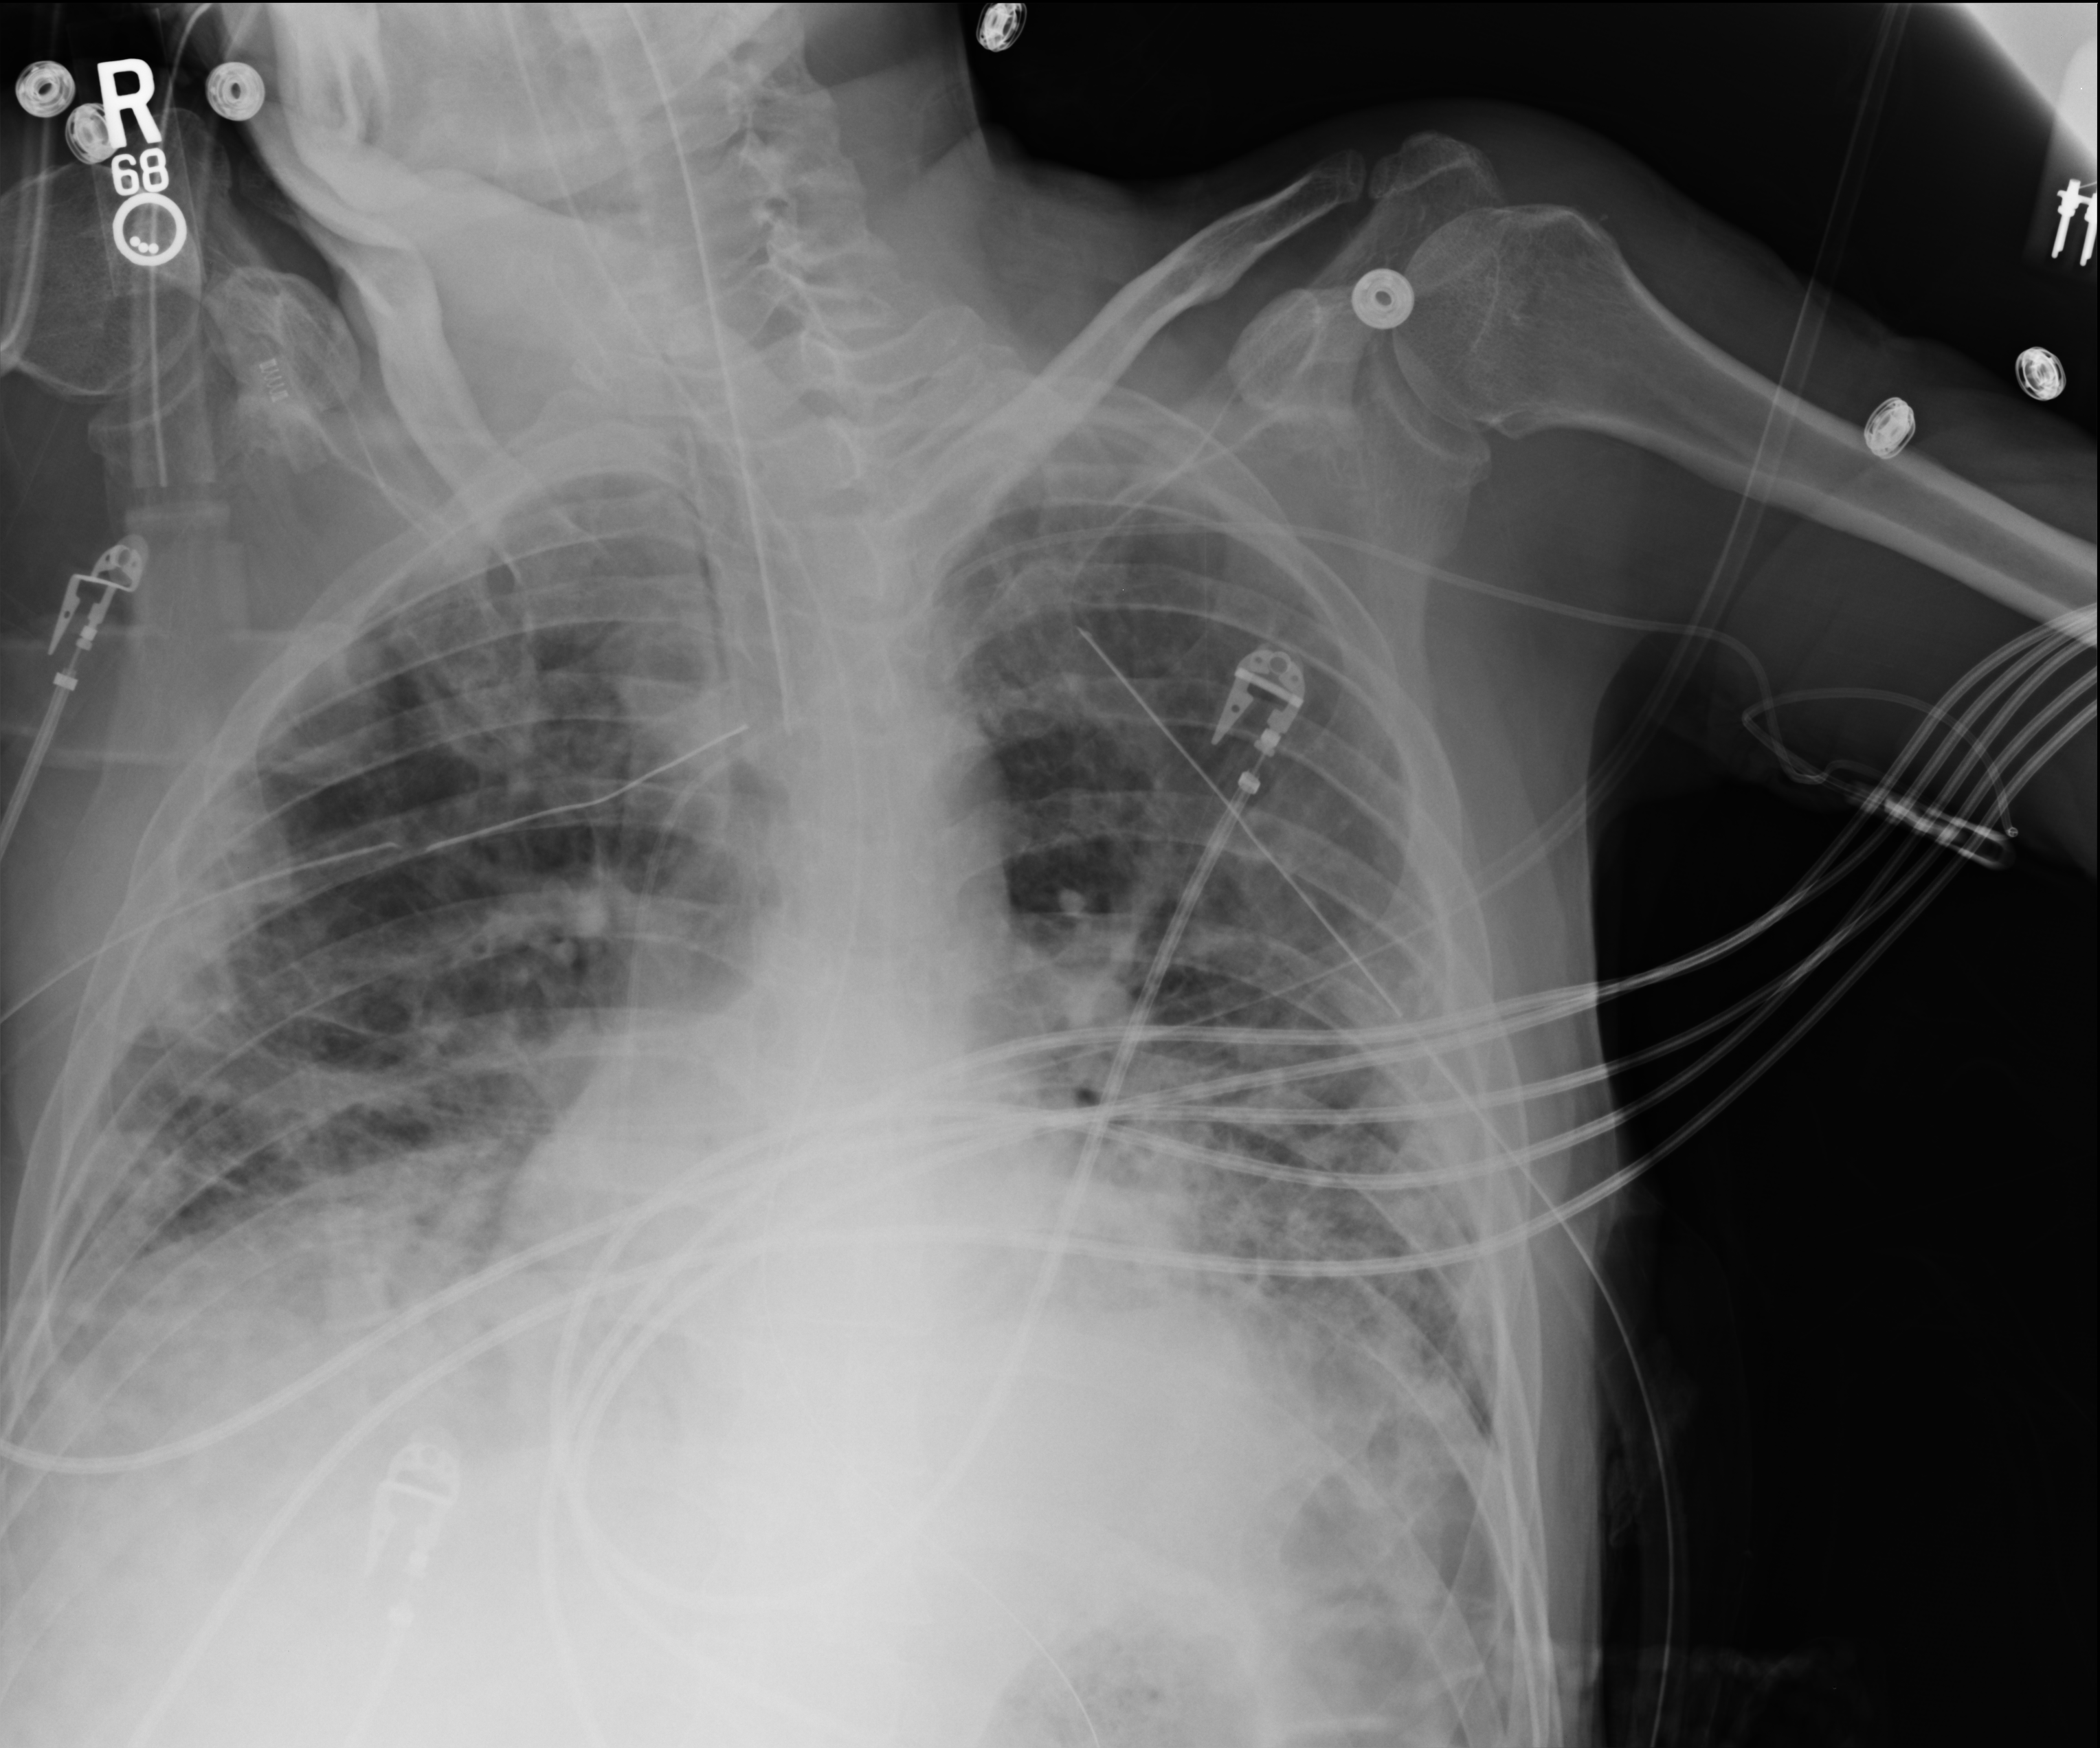
Portable chest radiograph, anteroposterior (AP) projection. Patient hospitalised with COVID-19; male, aged 18–59 years.
From the hospital-stay record, not from the radiograph (when in the stay this image was taken is not recorded):
- mechanically ventilated during this hospital stay: yes
- admitted to intensive care during this hospital stay: yes